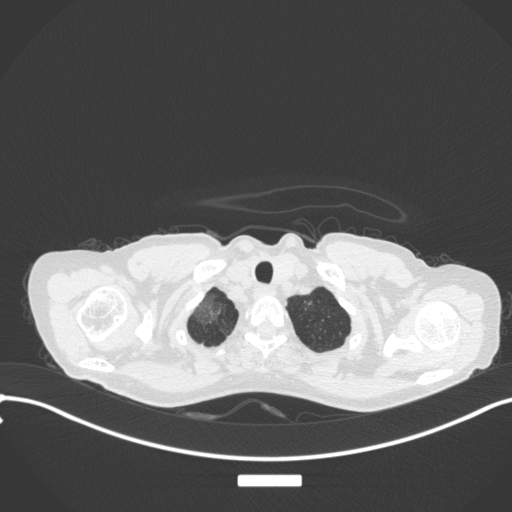
Chest CT, one axial slice; position 311 of 311 along the scan axis; 120 kVp; lung window (W 1500 / L -600 HU); 512 × 512 image matrix, field of view 400 × 400 mm. Female patient, age 59 years. Case-level facts recorded for this patient, not image findings: clinical TNM (as recorded): T3 N0 M0.
Annotated regions visible in this slice (rectangle marked by the reading radiologist):
- lung tumour (recorded histology: adenocarcinoma): bounding box <190,298,222,322> (left, top, right, bottom; pixels)